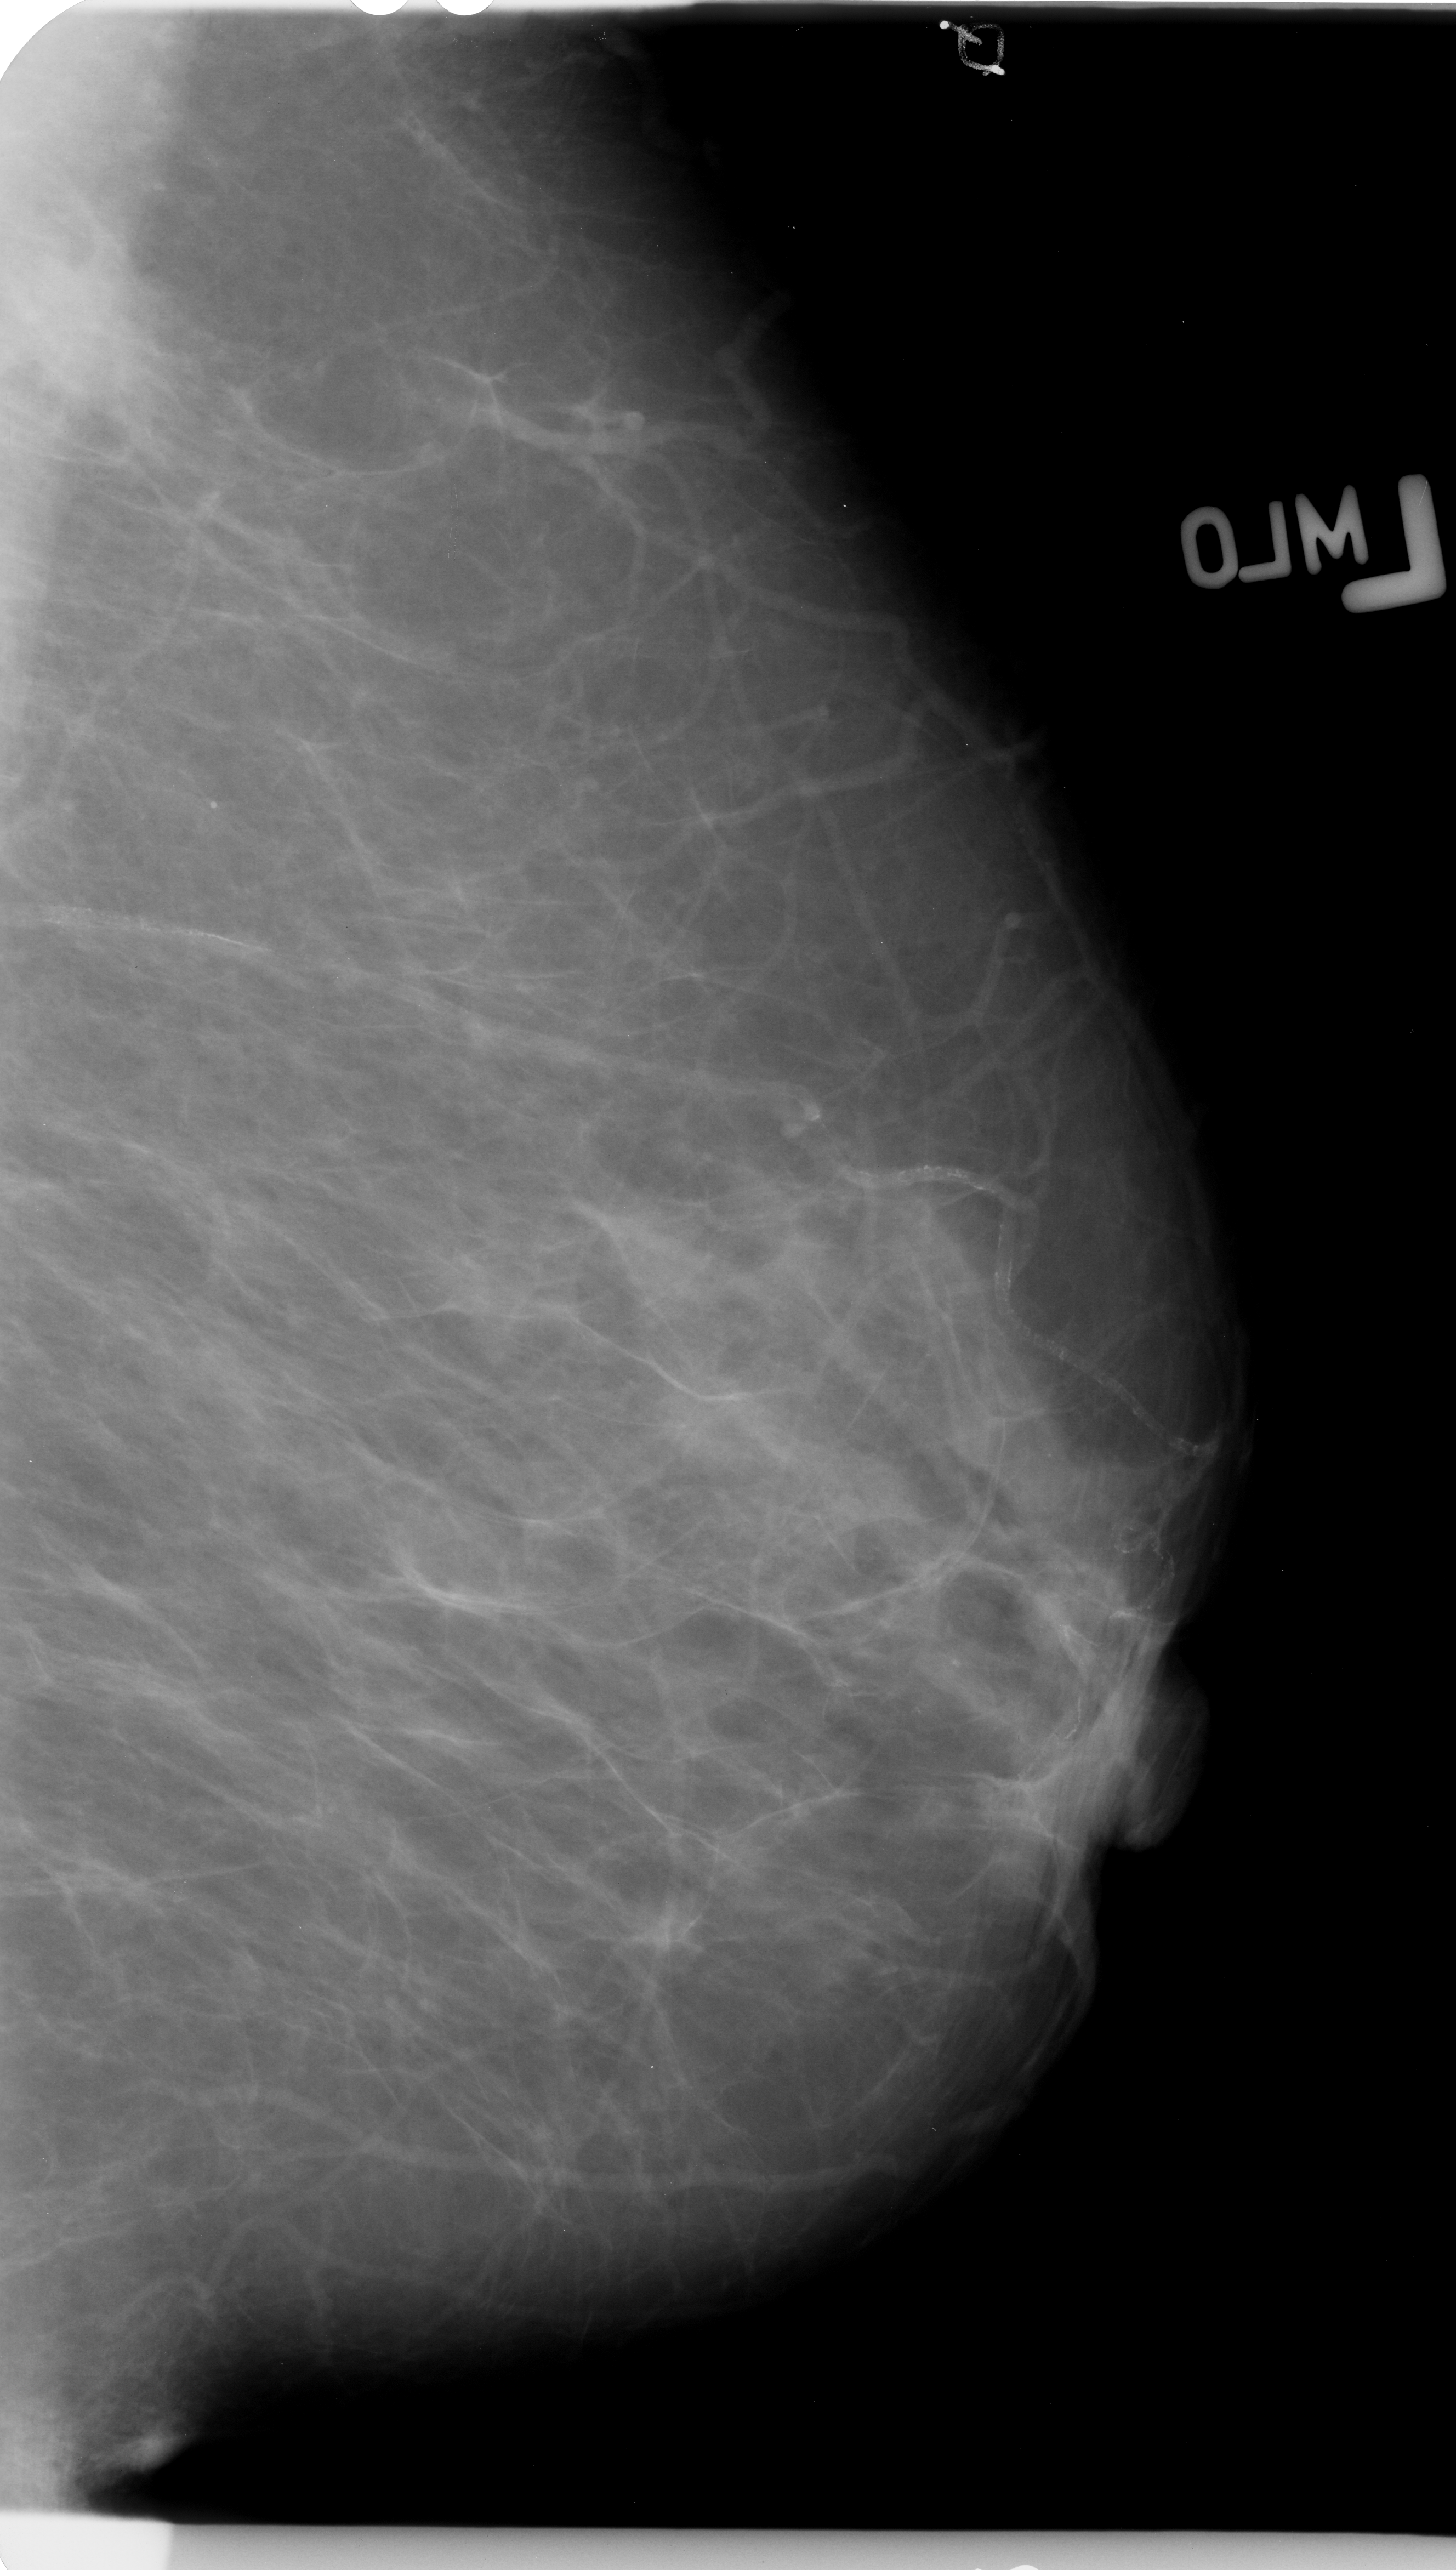
Scanned film-screen mammogram; left breast; mediolateral oblique (MLO) view; breast composition: scattered fibroglandular densities (BI-RADS density category 2 of 4); 1456 × 2570 image matrix.
Expert-marked regions of interest on this film, with their recorded descriptors:
- mass, shape irregular, margins spiculated; BI-RADS assessment category 4; subtlety rating 4 on a 1 (subtle) to 5 (obvious) scale; pathology (as recorded): malignant: bounding box <0,209,182,445> (left, top, right, bottom; pixels)